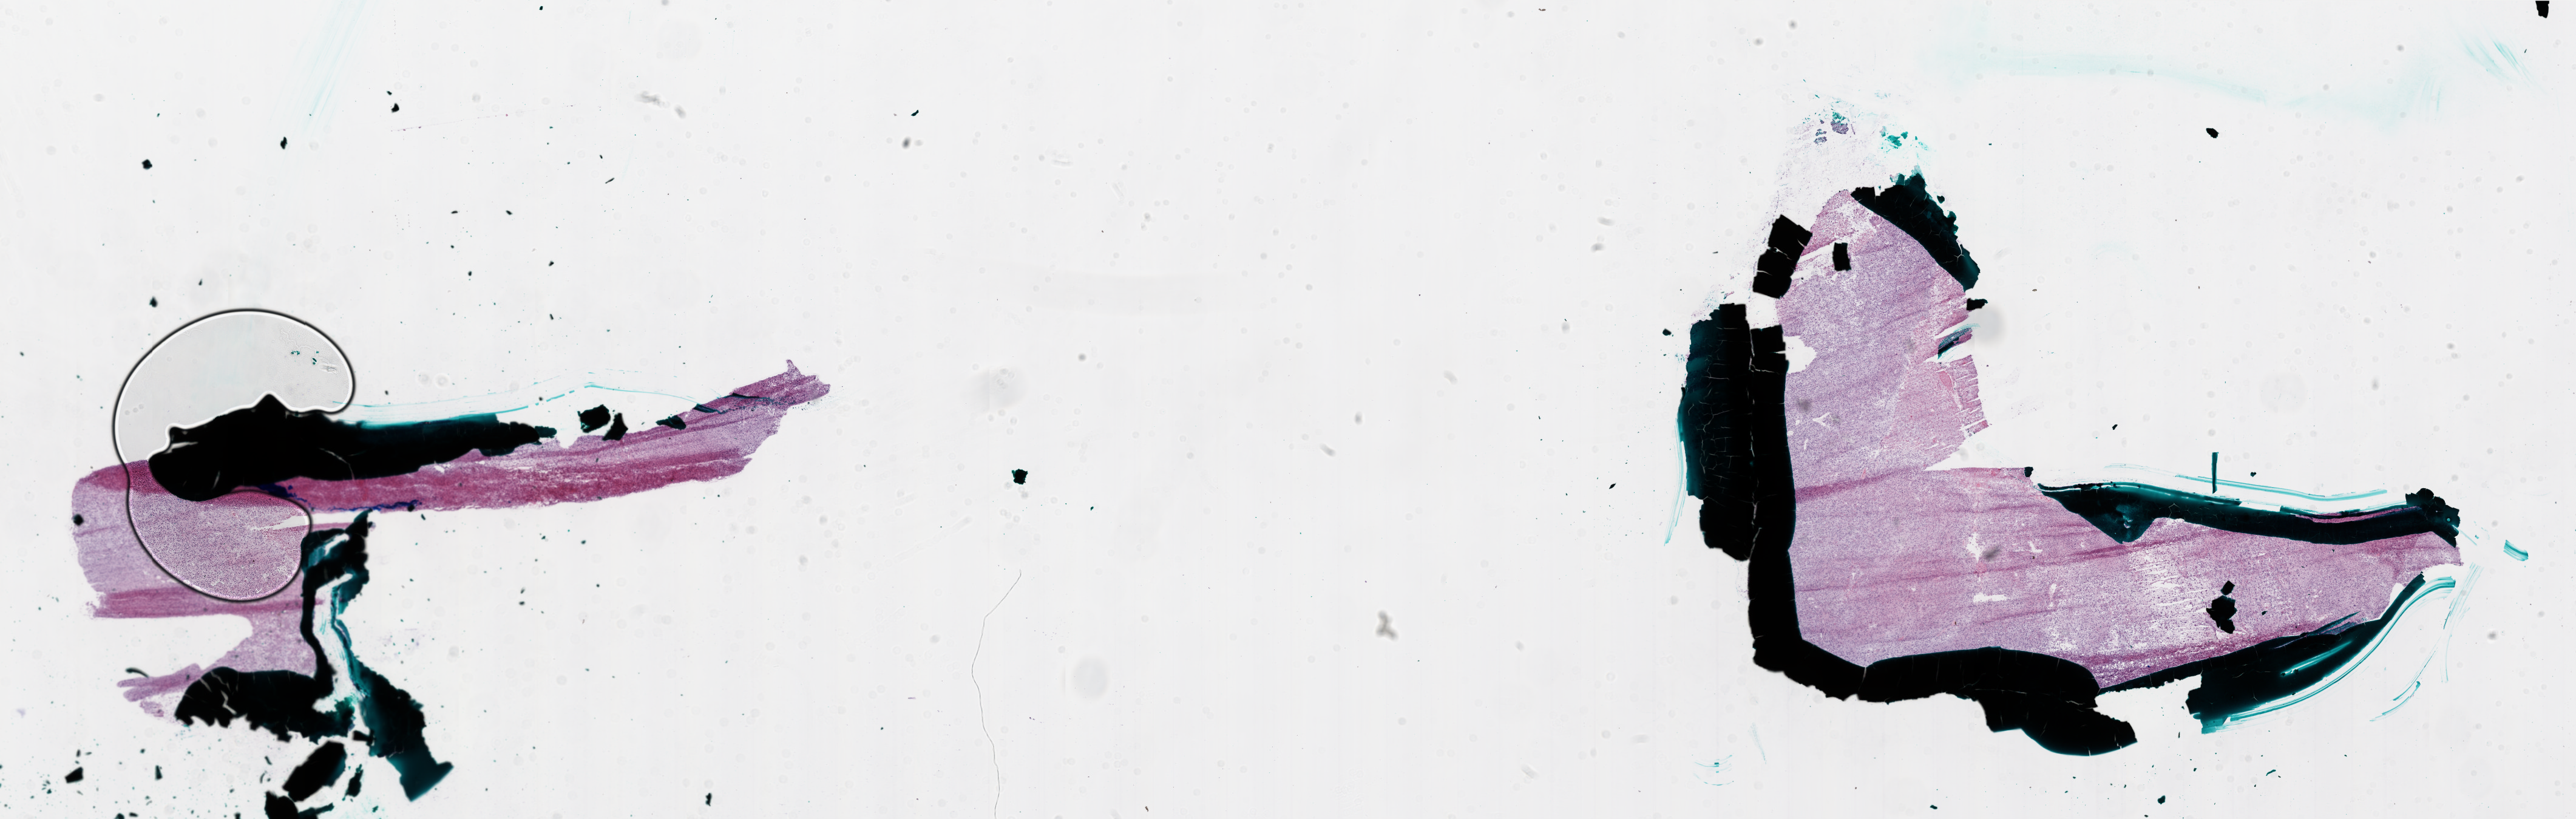
Whole-slide histology image, Hematoxylin and eosin (H&E) stained — a low-resolution overview of the entire scanned area, about 34.0 x 10.8 mm; frozen section from the top of the tissue portion; brain, primary tumour sample. Male patient; age at initial diagnosis 57 years.
Pathologic diagnosis: Glioblastoma.